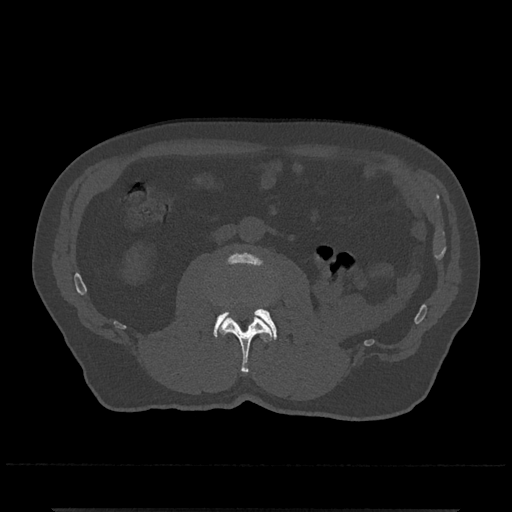
CT including the spine, one axial slice; position 264 of 797 along the scan axis; 120 kVp; bone window (W 1800 / L 400 HU); 0.5 mm slice thickness; 512 × 512 image matrix, field of view 393 × 393 mm. Male patient, age 67 years. Case-level facts recorded for this patient, not image findings: primary cancer: prostate.
Annotated regions visible in this slice (semi-automatically segmented with operator editing):
- L2 vertebra: bounding box (x1, y1, x2, y2) in pixels: (219, 315, 272, 374)
- L3 vertebra: (214, 253, 277, 340)